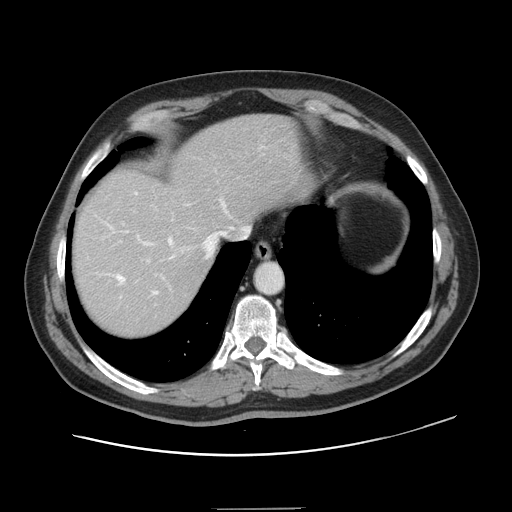
Contrast-enhanced abdominal CT, one axial slice. Position 122 of 143 along the scan axis. 120 kVp. Intravenous contrast given. Soft-tissue window (W 400 / L 40 HU). 2.5 mm slice thickness. 512 × 512 image matrix, field of view 402 × 402 mm. Male patient, age 62 years. From the clinical record (not read from this slice): diagnosis: colorectal cancer liver metastases, imaged before liver resection; multiple liver metastases: yes; largest metastasis: 2.7 cm; disease in both lobes: no.
Structures marked on this image (manually delineated by an expert):
- hepatic veins: bounding box (x1, y1, x2, y2) in pixels: (109, 192, 249, 295)
- liver: (74, 114, 302, 337)
- planned liver remnant (the part of the liver to remain after resection): (74, 115, 302, 293)
- portal vein (with intrahepatic branches): (120, 223, 164, 279)